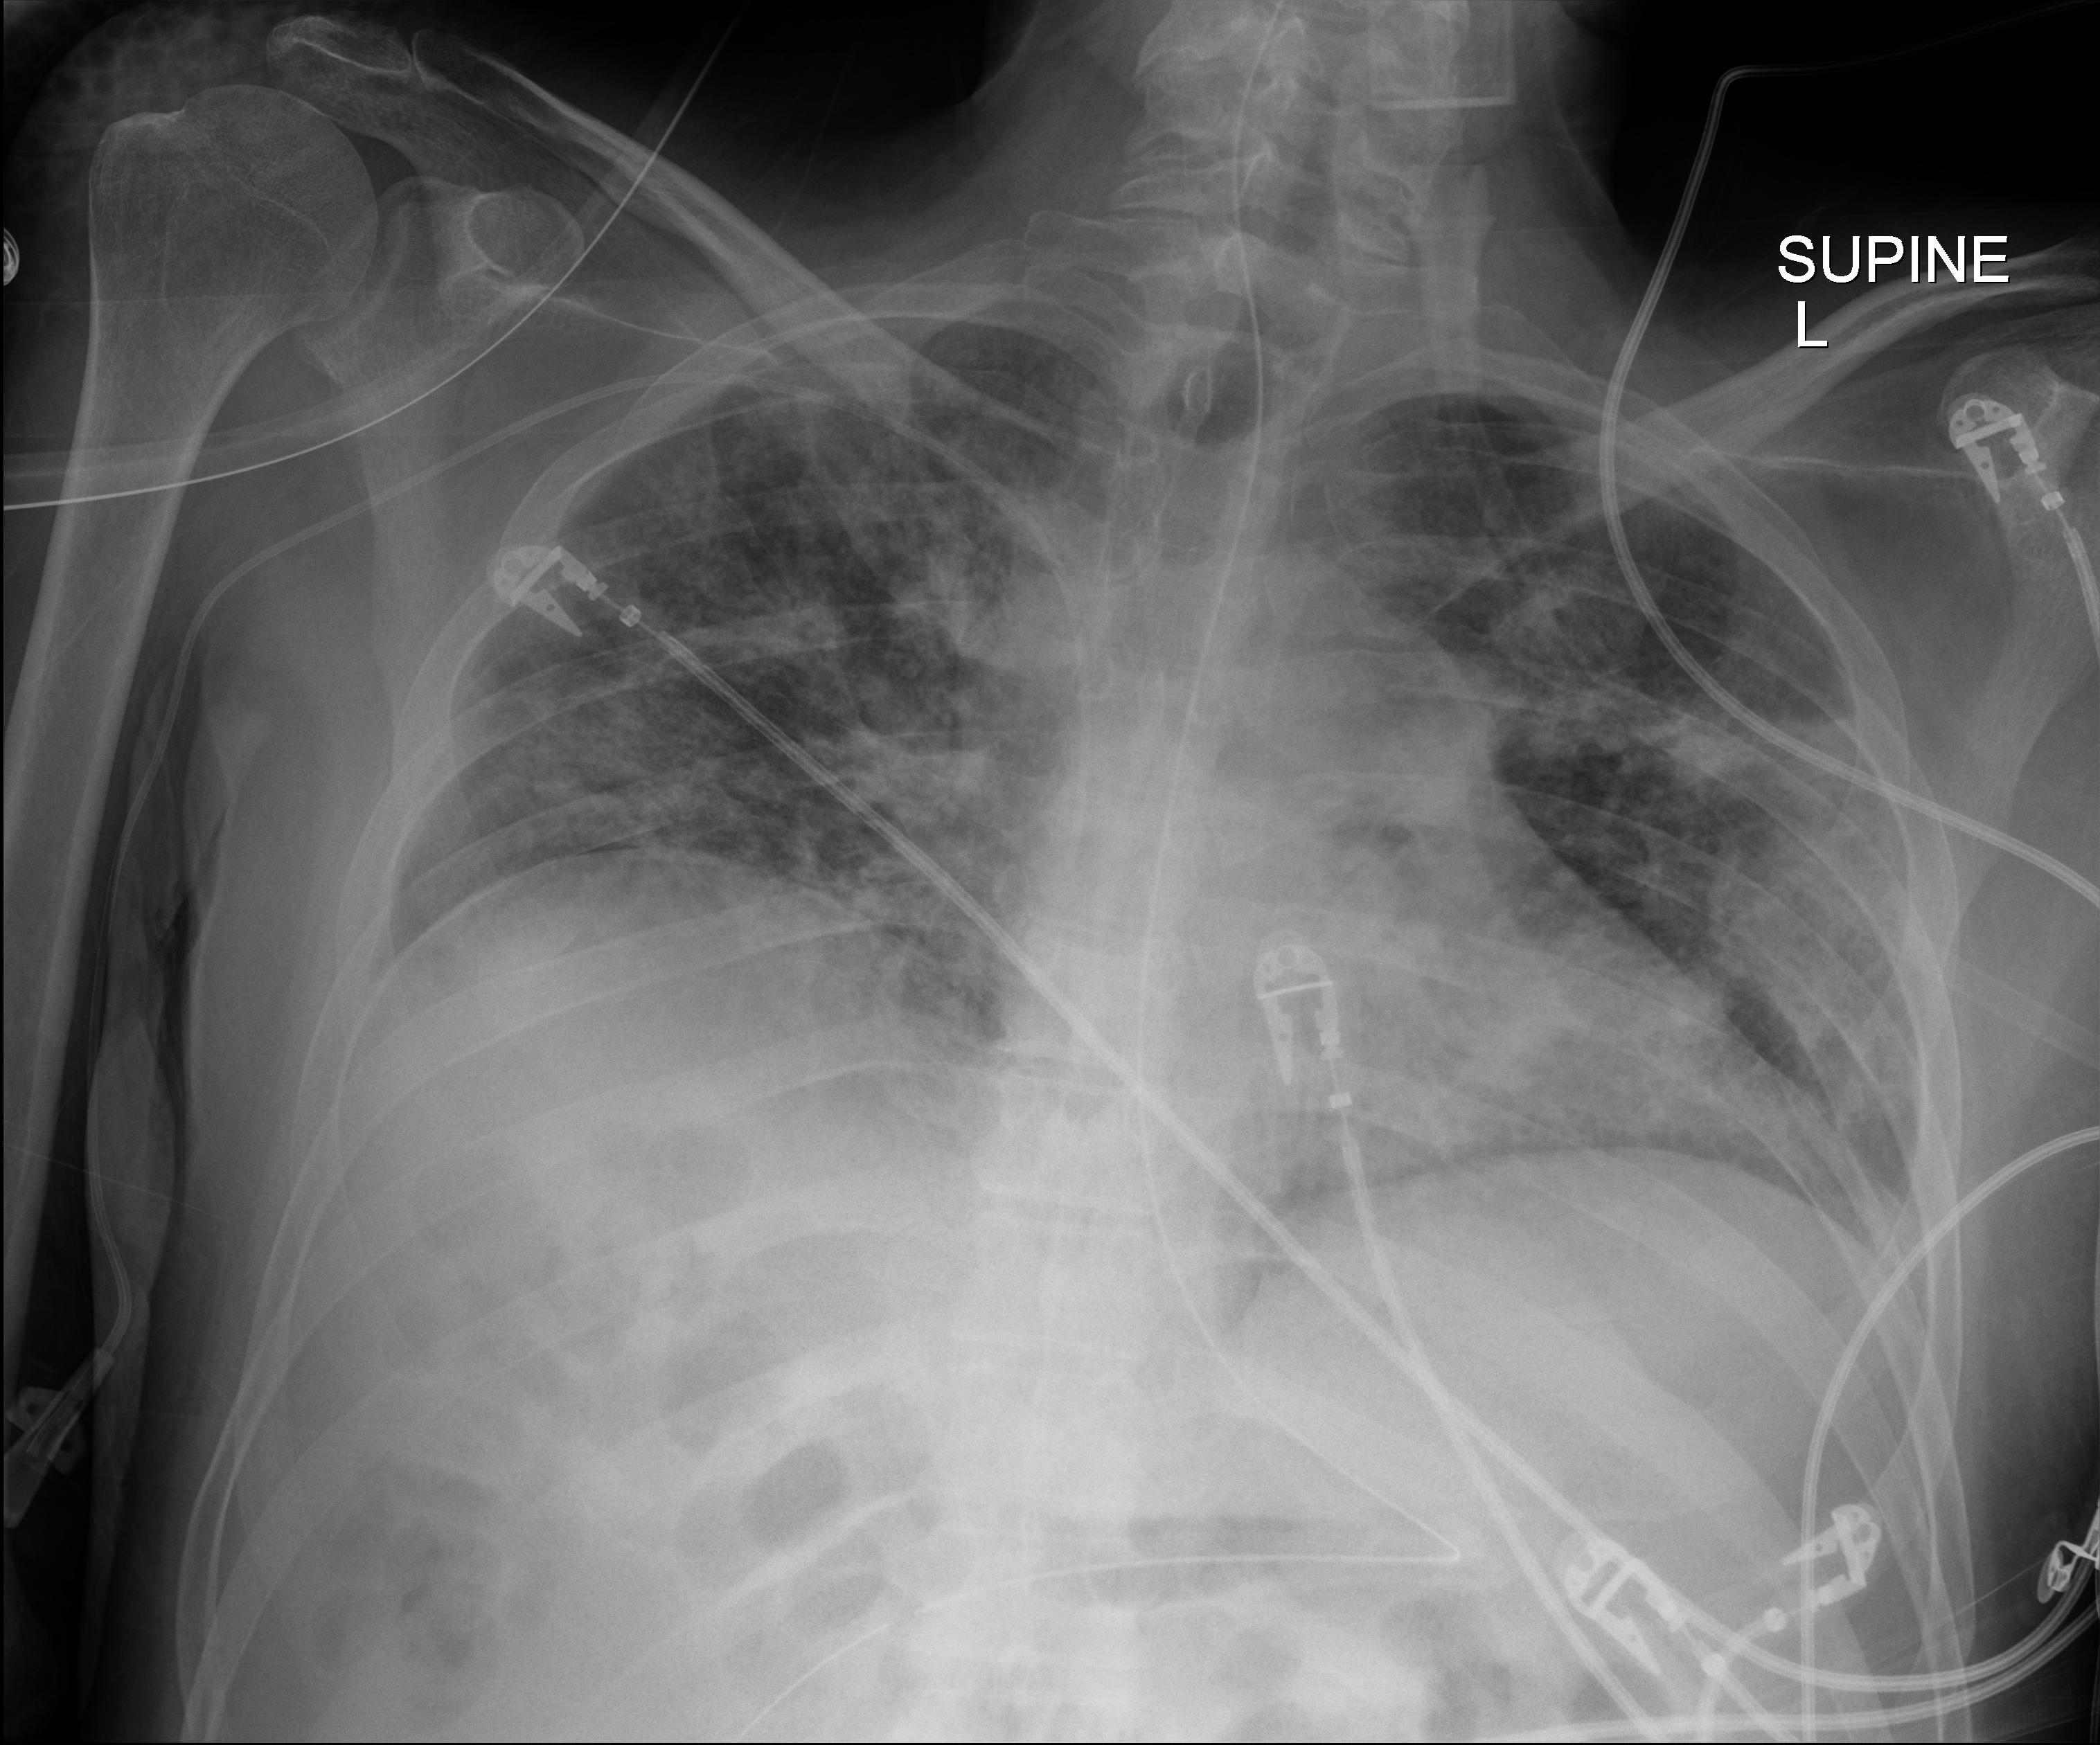
Portable chest radiograph, anteroposterior (AP) projection. Male patient hospitalised with COVID-19, age 18–59 years.
Admission-level facts for this patient (not findings on this image; timing relative to this image not recorded): admitted to intensive care during this hospital stay: yes; diabetes (admission record): no; mechanically ventilated during this hospital stay: yes.